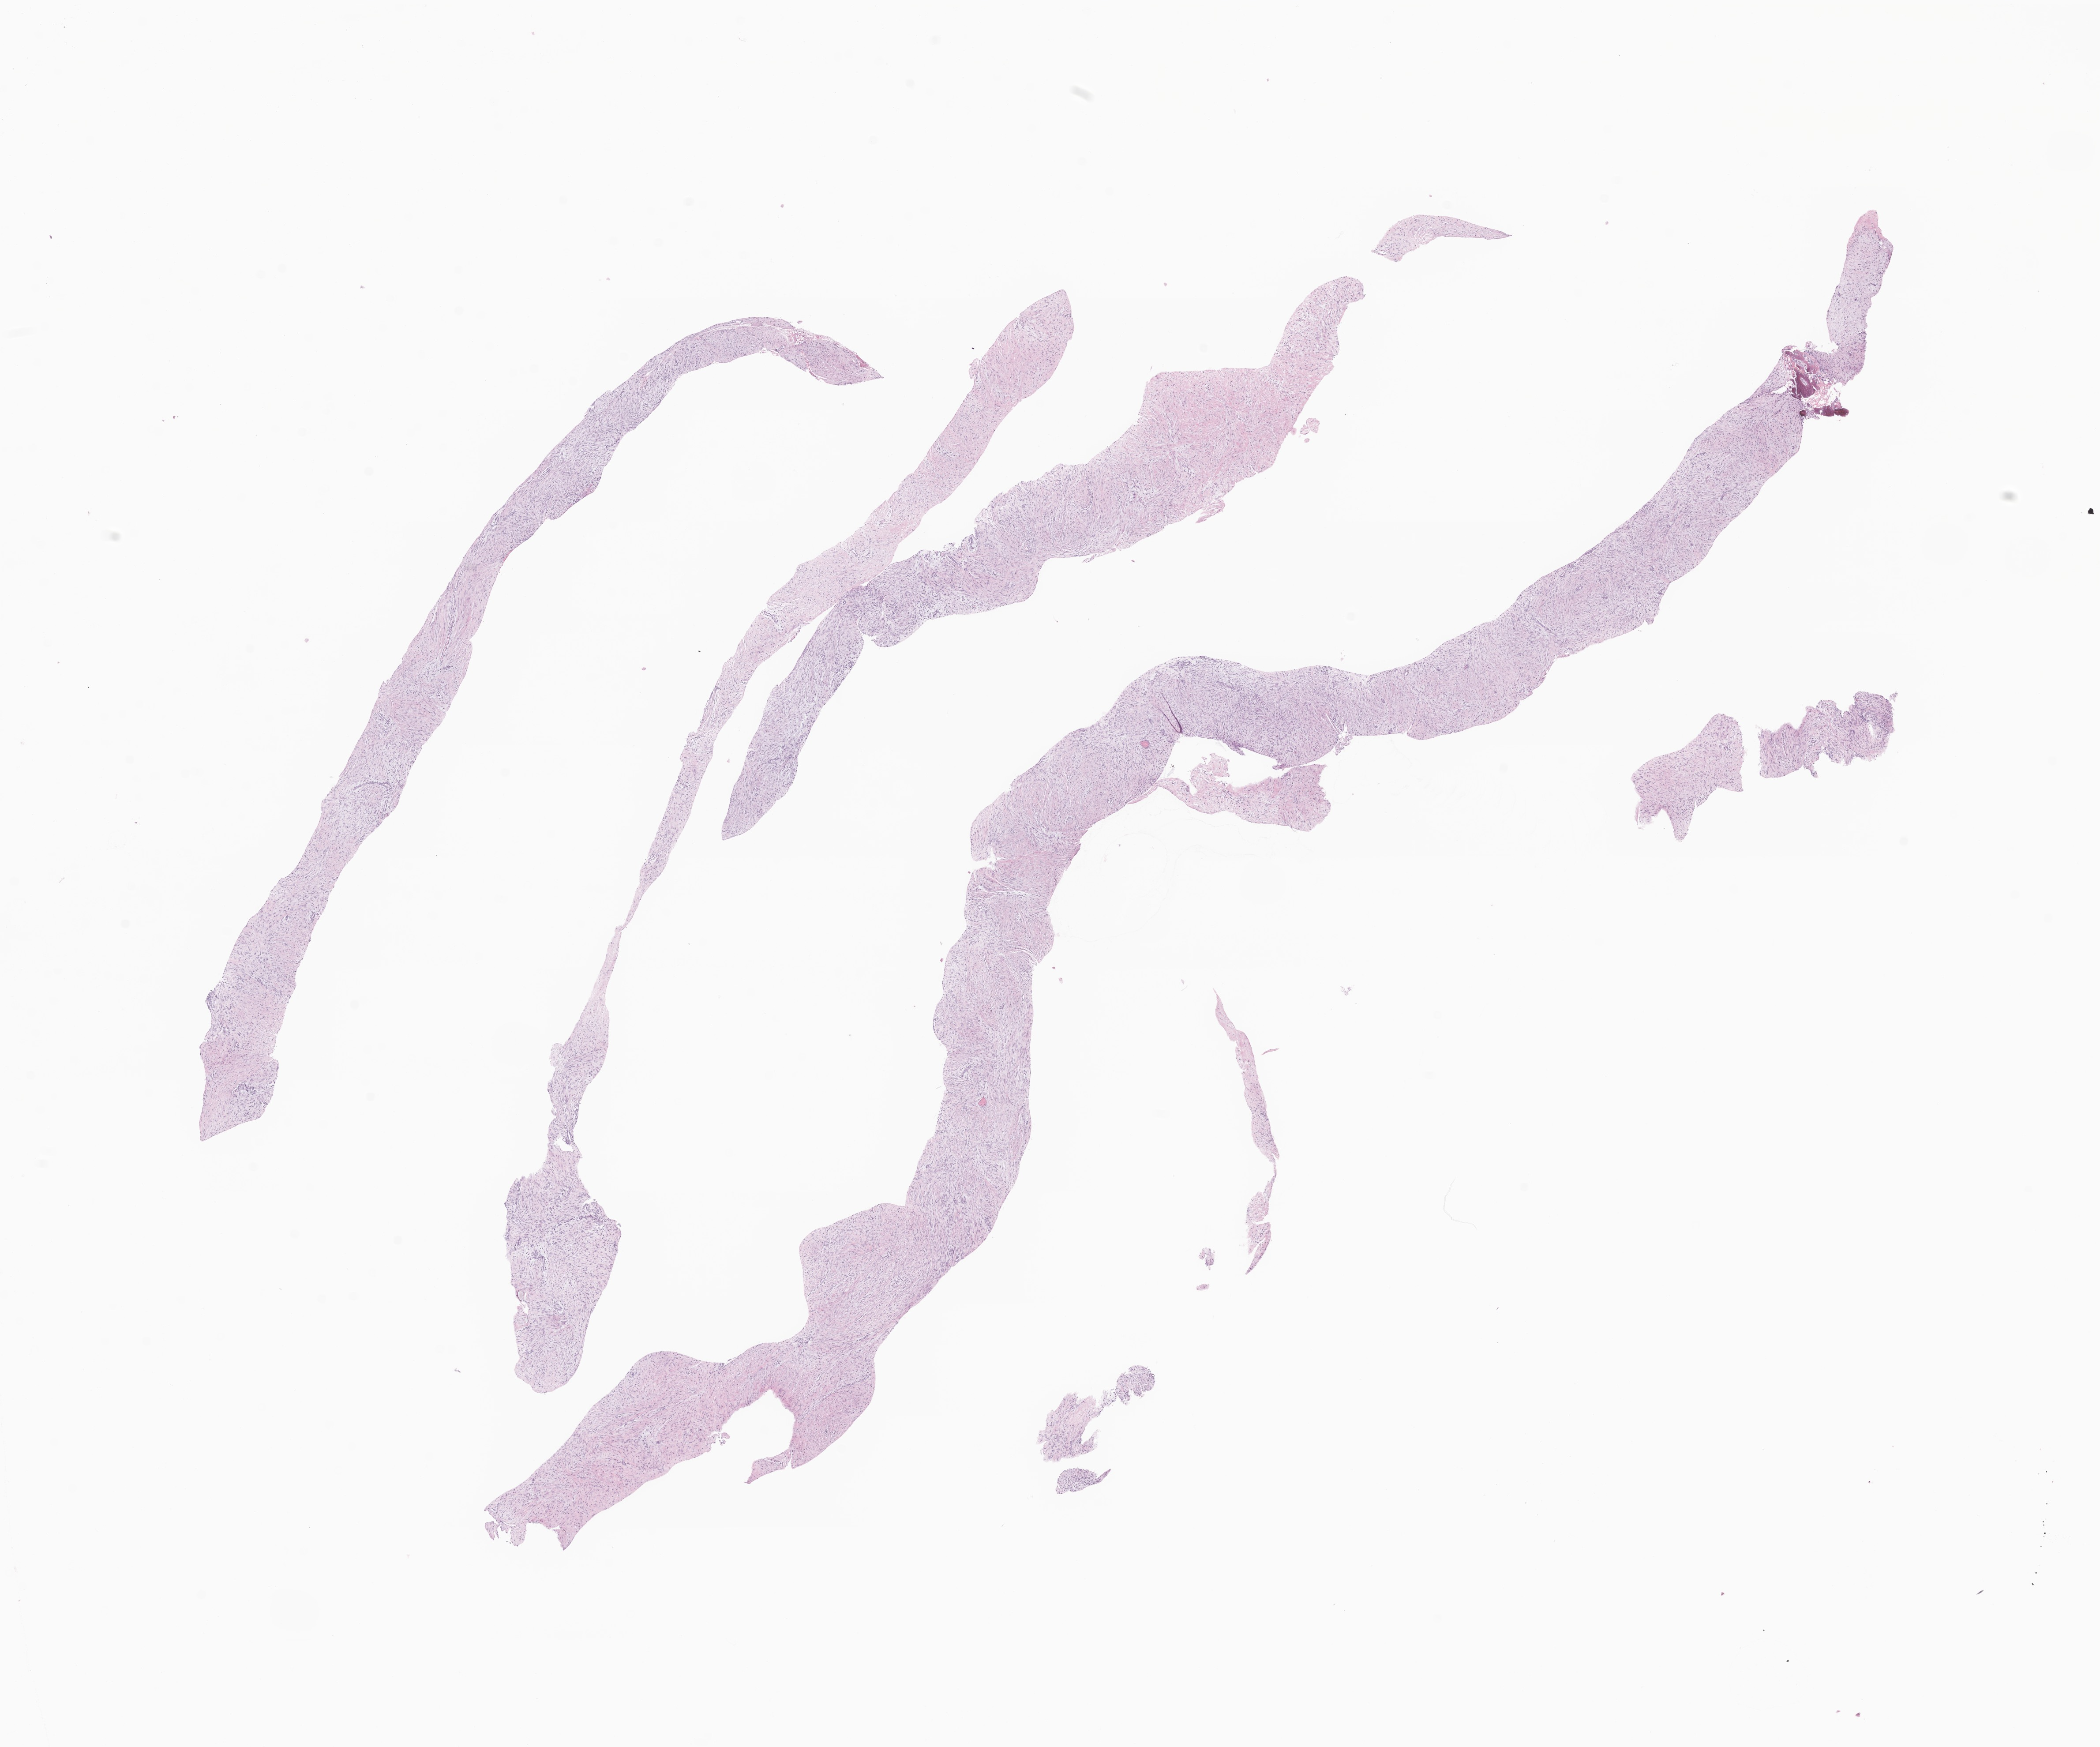
Whole-slide image, H&E stain of tumor tissue from the submandibular gland, shown as a low-resolution overview of the whole scanned area (about 20.1 x 16.7 mm), formalin-fixed paraffin-embedded section. Male patient, age 139 months (11 years 7 months).
Diagnosis: Fibroma, NOS.